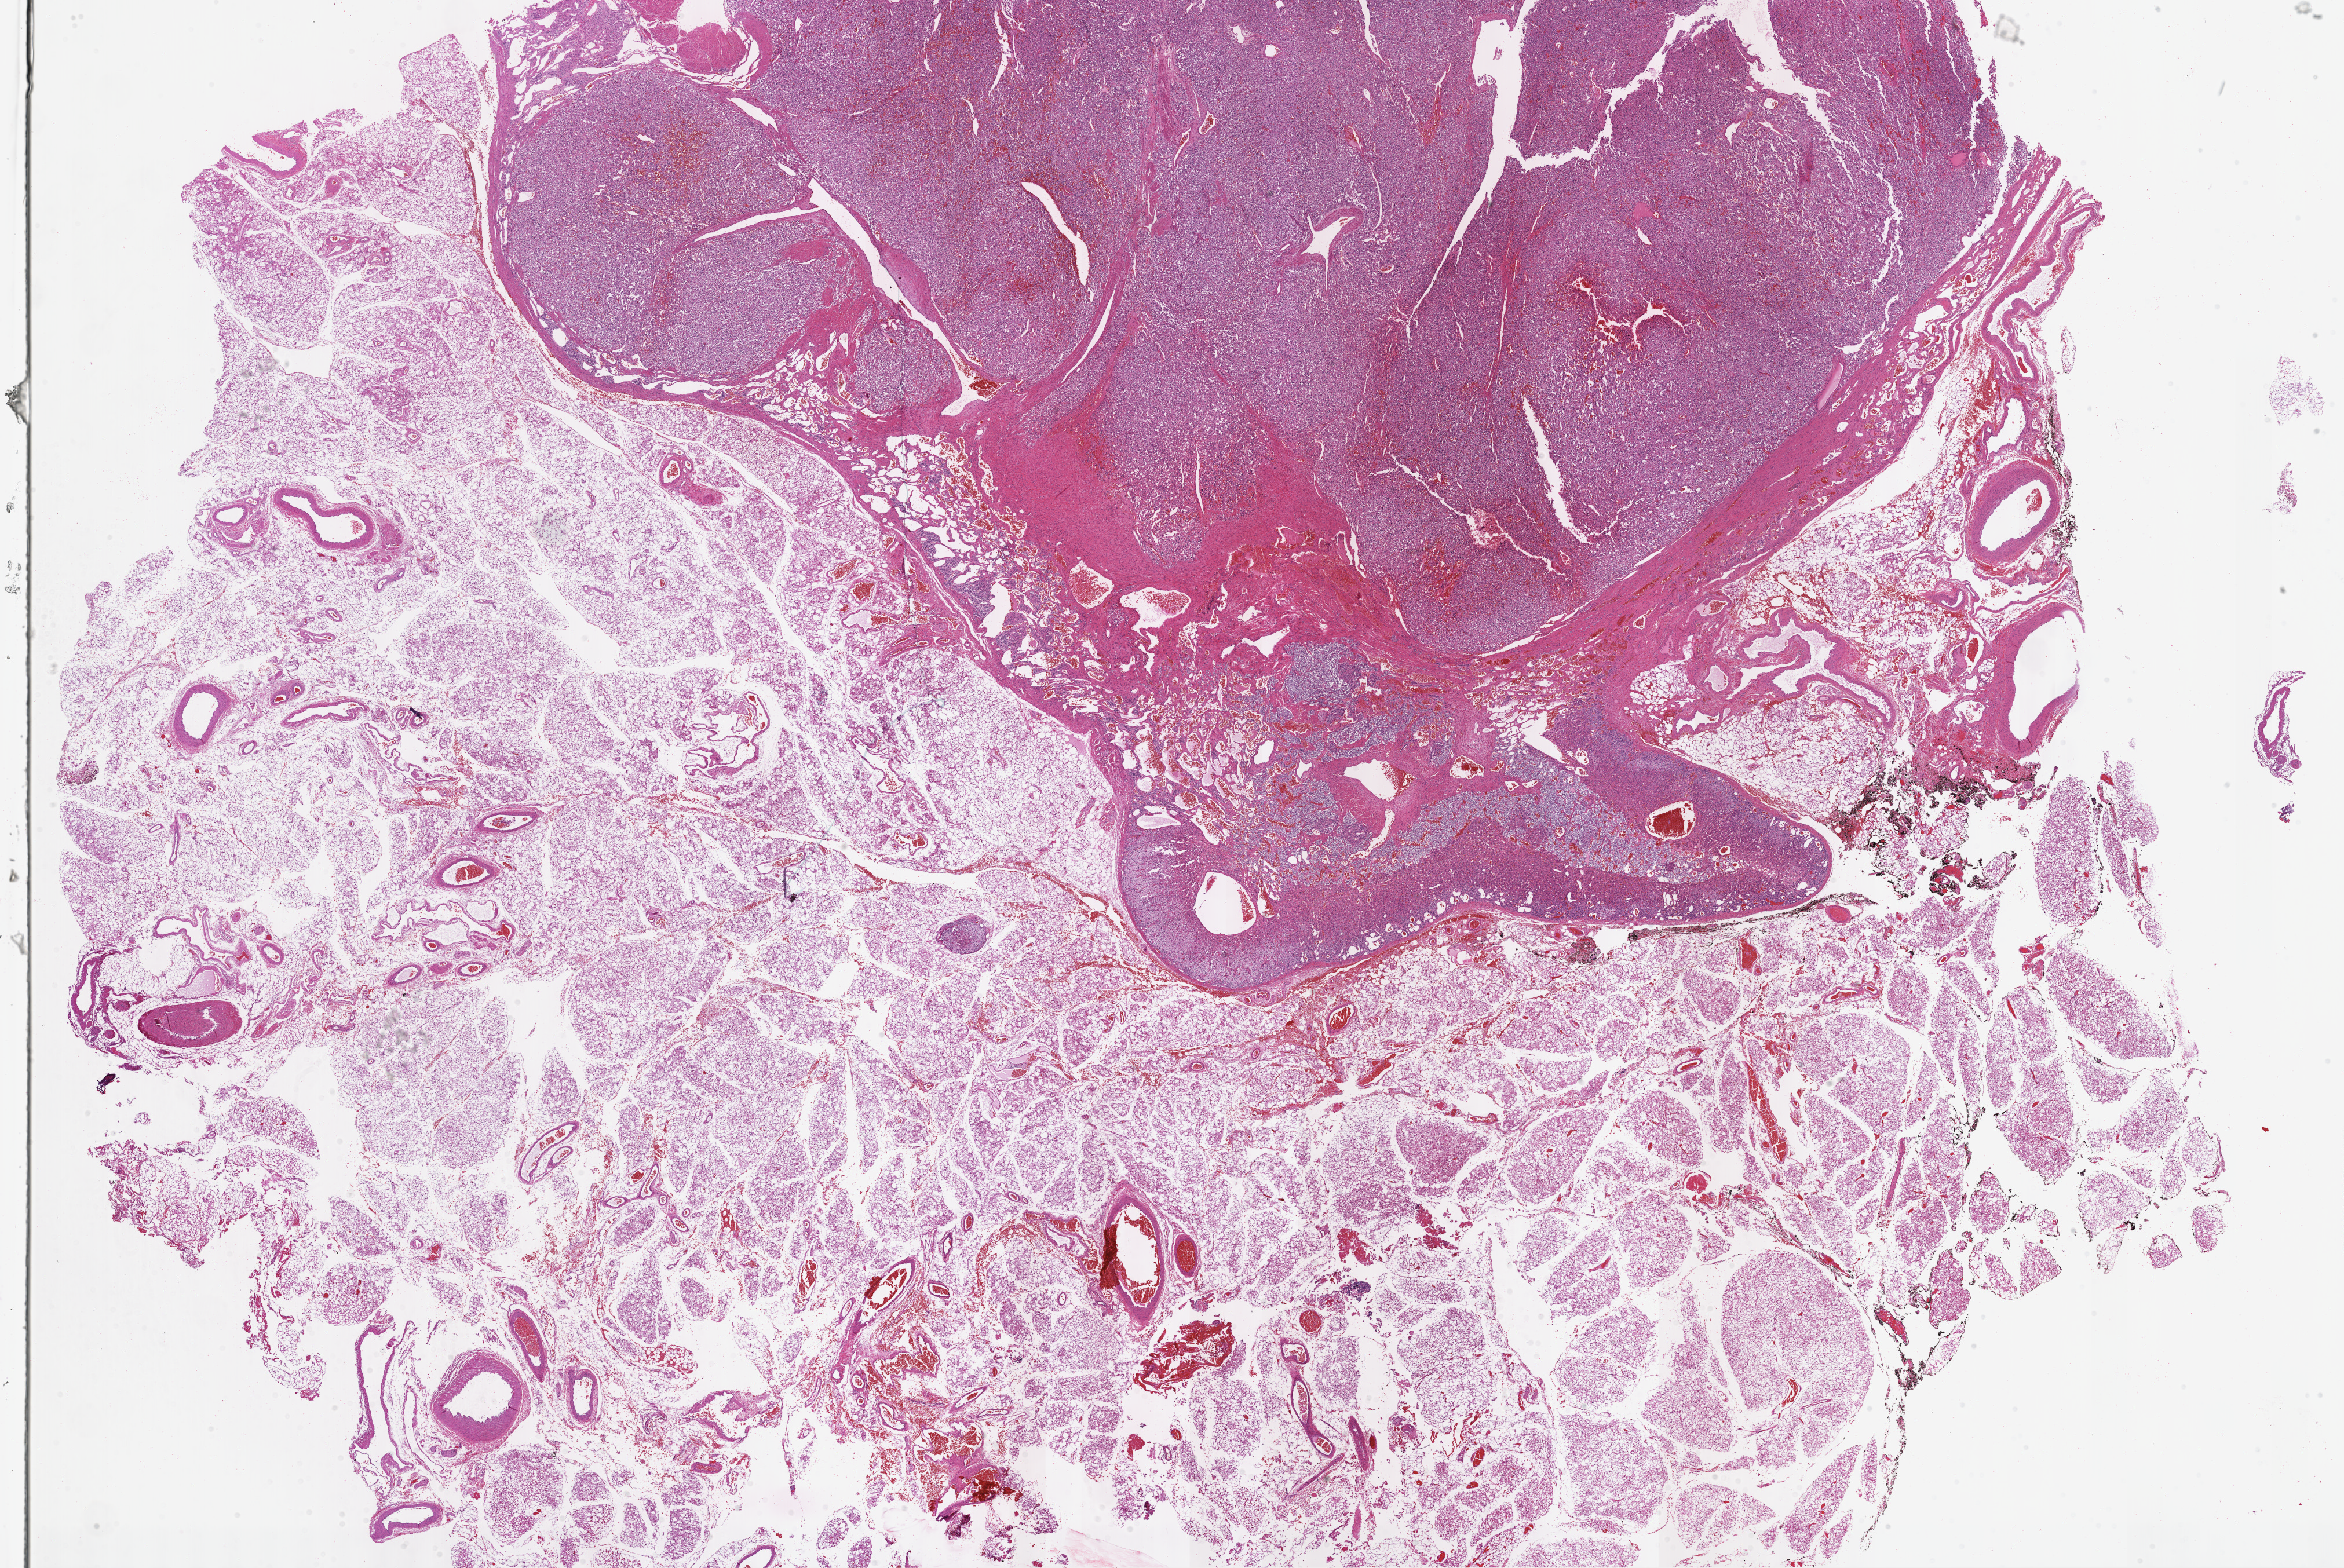
Digitized H&E-stained tissue section (whole slide) — whole scanned area (about 32.7 x 21.9 mm) shown as a low-resolution overview. Formalin-fixed paraffin-embedded (FFPE) diagnostic section. Adrenal gland, primary tumour sample. Patient: male, age at initial diagnosis 31 years.
- laterality: bilateral
- histologic diagnosis: Pheochromocytoma, NOS